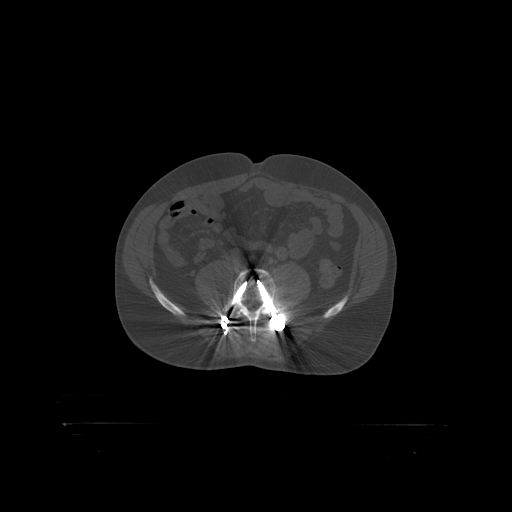
CT including the spine, one axial slice; position 211 of 399 along the scan axis; reconstruction kernel STANDARD; 120 kVp; bone window (W 1800 / L 400 HU); 1.25 mm slice thickness; 512 × 512 image matrix, field of view 650 × 650 mm. Male patient, age 46 years. From the clinical record (not read from this slice): primary cancer: skin.
Outlined on this slice (semi-automatic segmentation, software-assisted and operator-edited):
- L4 vertebra: bounding box [x1, y1, x2, y2] px = [238, 315, 243, 317]
- L5 vertebra: [223, 270, 290, 319]